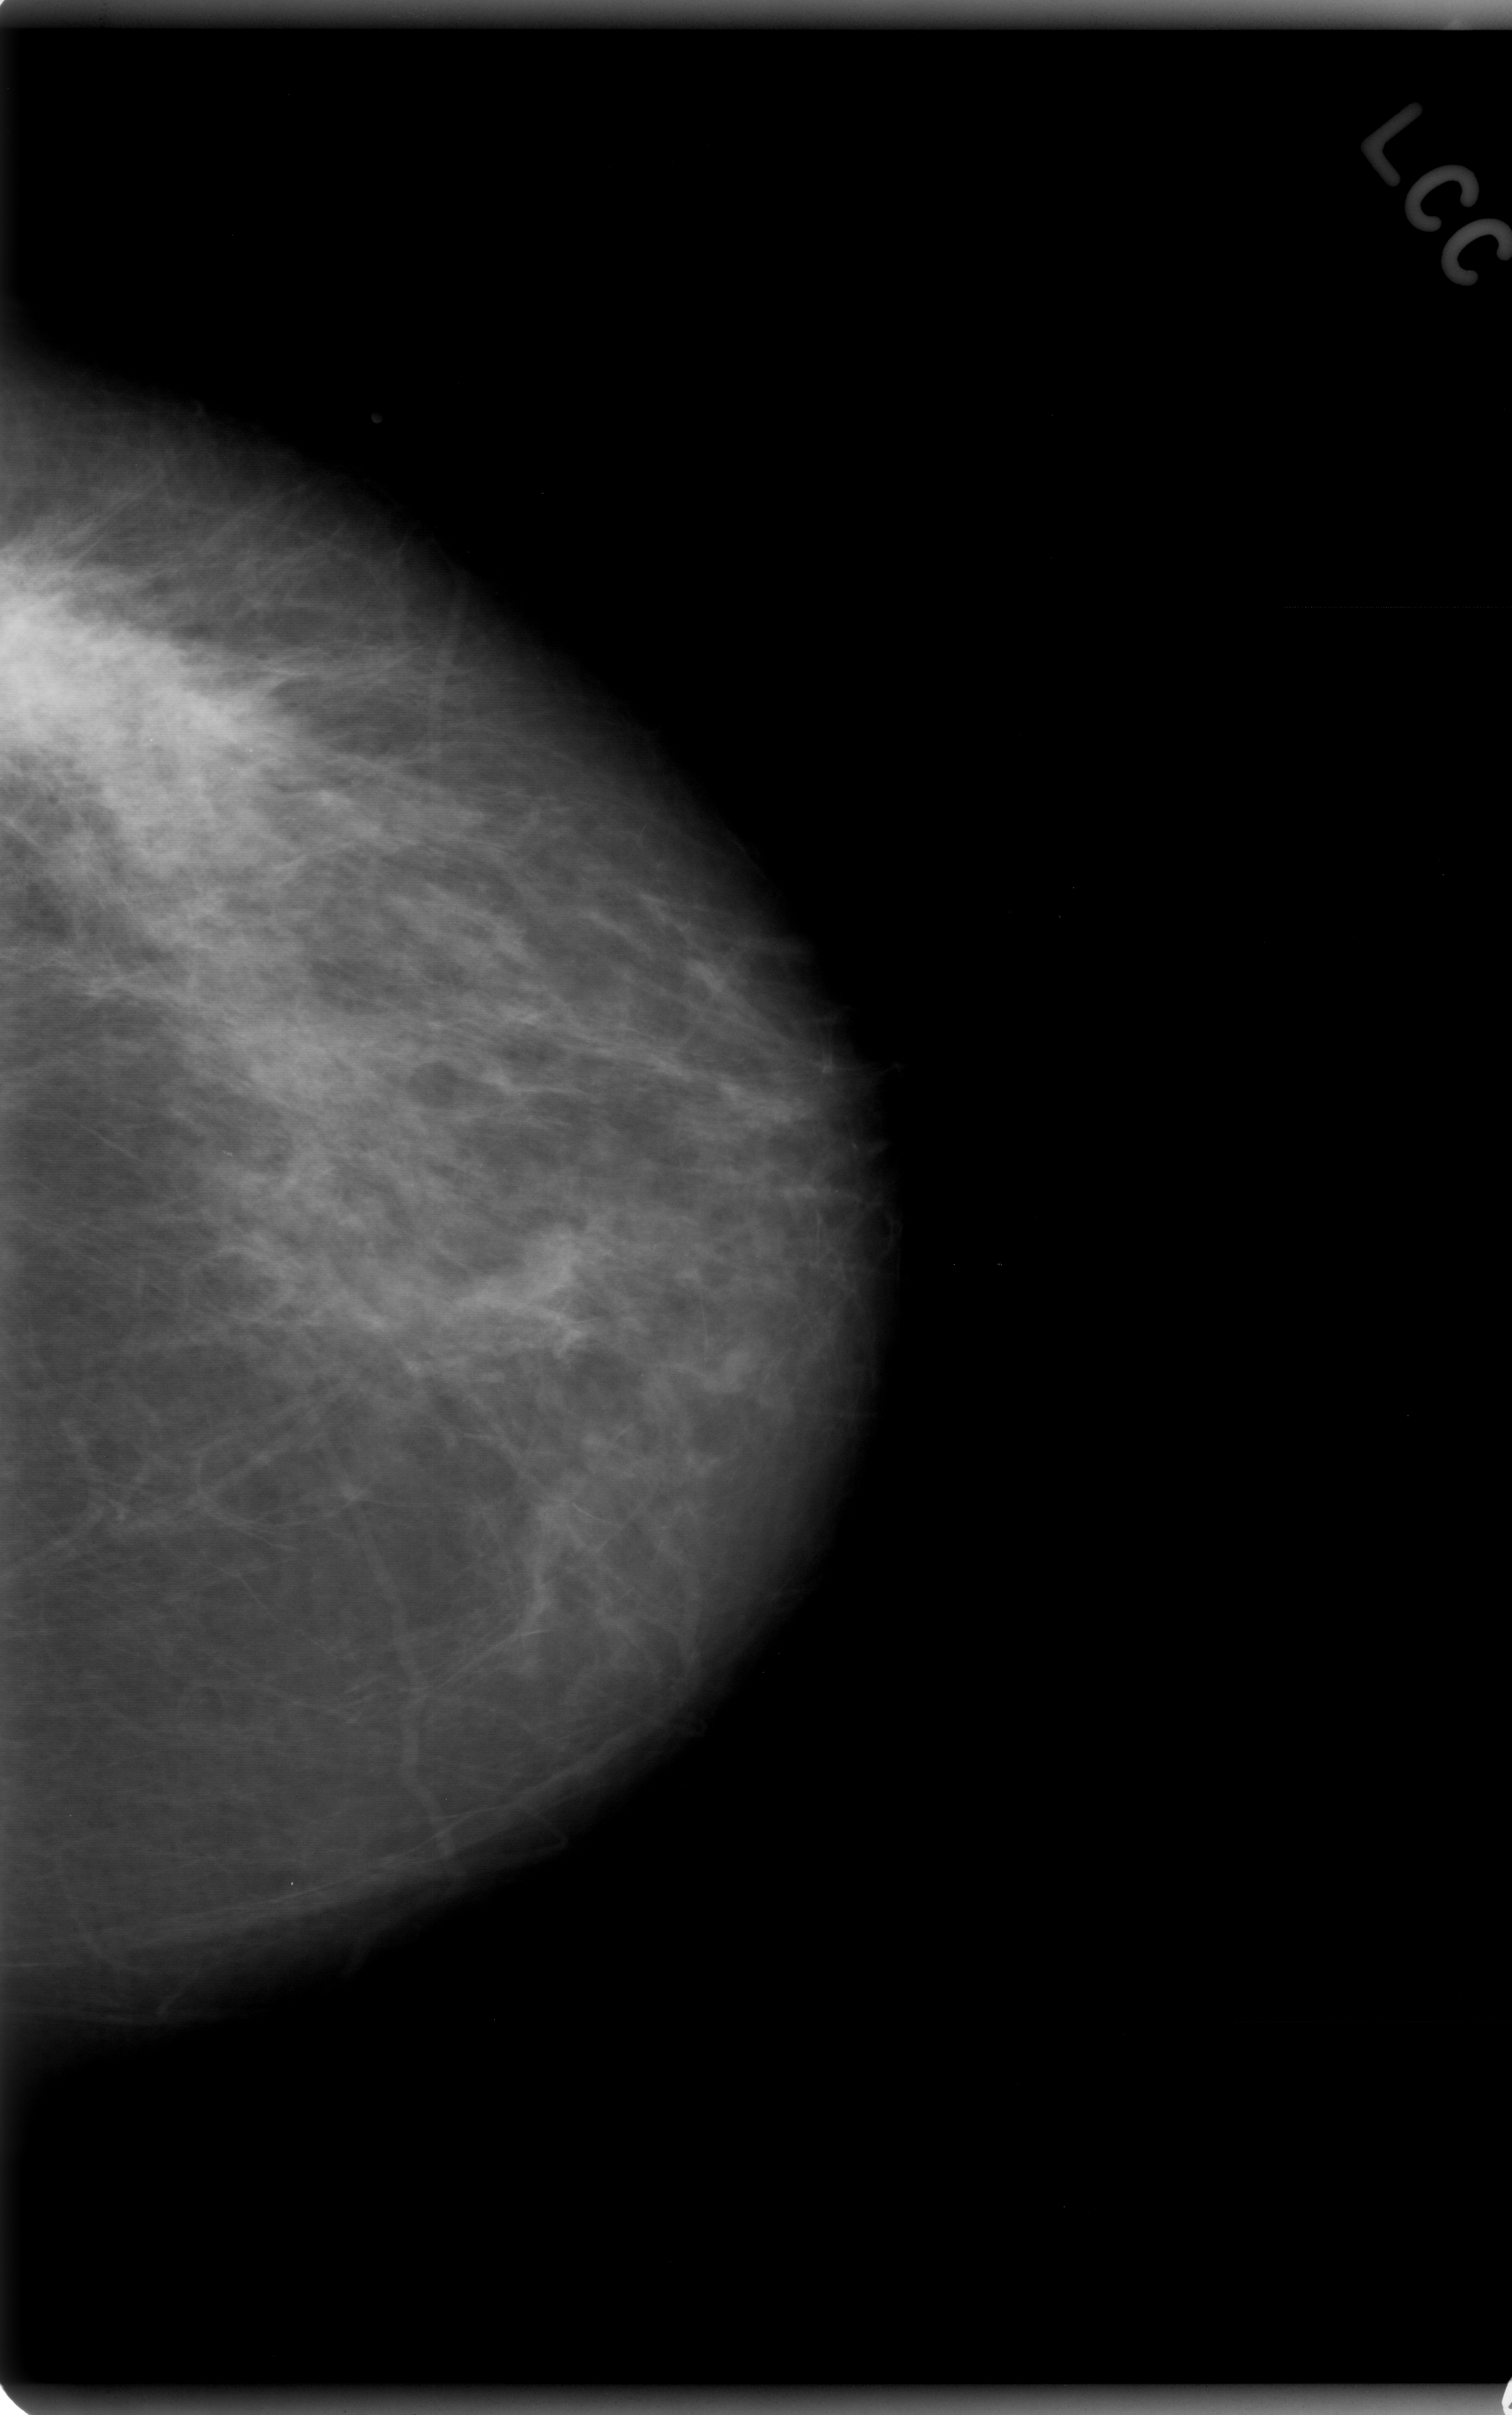
Scanned film-screen mammogram; left breast; craniocaudal (CC) view; breast composition: scattered fibroglandular densities (BI-RADS density category 2 of 4); 1512 × 2415 image matrix.
Marked abnormalities (boxes around the expert regions of interest):
- calcifications, morphology pleomorphic, distribution regional; BI-RADS assessment category 4; pathology result (as recorded, not read from the image): malignant: bounding box [x1, y1, x2, y2] px = [0, 492, 659, 1331]